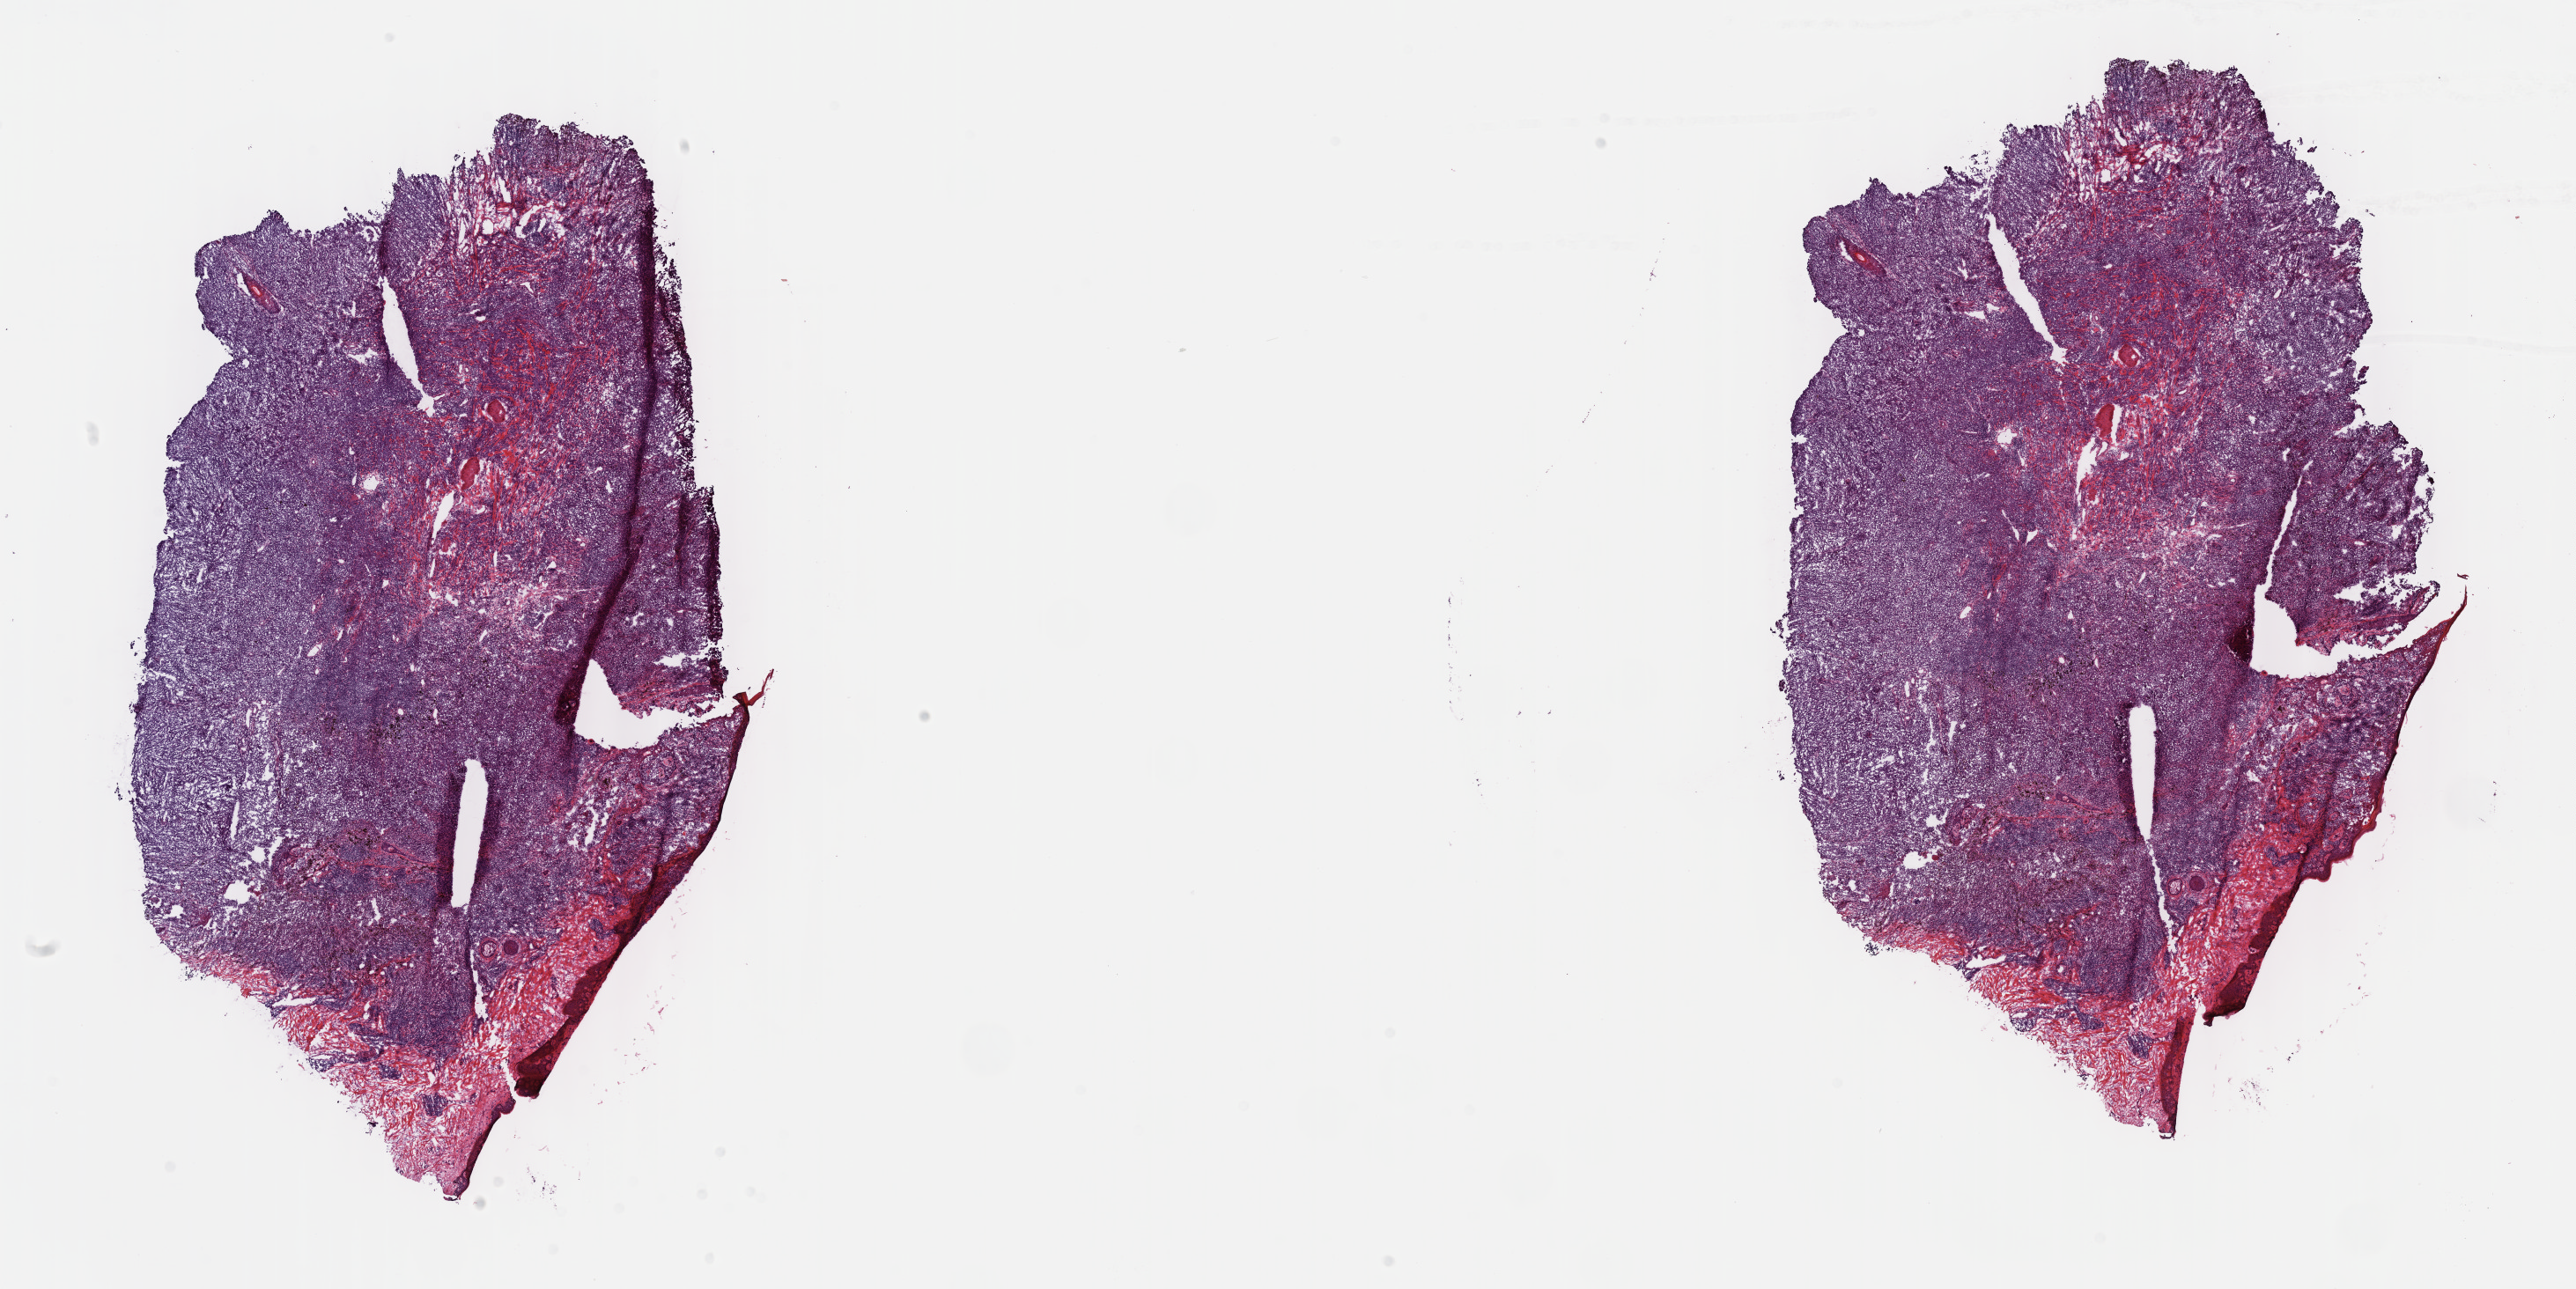
Digitized H&E tissue section (whole slide), shown as a low-resolution overview of the whole scanned area (about 23.7 x 11.8 mm). Frozen section from the top of the tissue portion. Sample: primary tumour, skin. Male, age 62 years at initial diagnosis. Slide review estimates, as recorded: tumour cells 85%, tumour nuclei 75%, normal cells 15%, stromal cells 0%, necrosis 0%. Infiltration values recorded for this section: lymphocyte infiltration 2%, monocyte infiltration 0%, neutrophil infiltration 0%.
* AJCC pathologic stage: IIB (7th edition)
* histologic diagnosis: Epithelioid cell melanoma